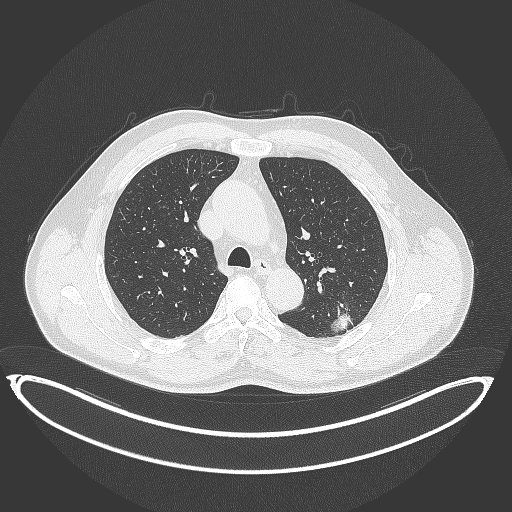
Chest CT, one axial slice. Slice 249 of 399 in the series (ordered by position). Reconstruction kernel B70f. Lung window (W 1500 / L -600 HU). 512 × 512 image matrix, field of view 469 × 469 mm. Male patient, age 58 years. From the clinical record (not read from this slice): clinical TNM (as recorded): T1c N0 M0.
Structures marked on this image (bounding box drawn by a radiologist):
- lung tumour (recorded histology: adenocarcinoma): bounding box (x1, y1, x2, y2) in pixels: (325, 308, 360, 336)